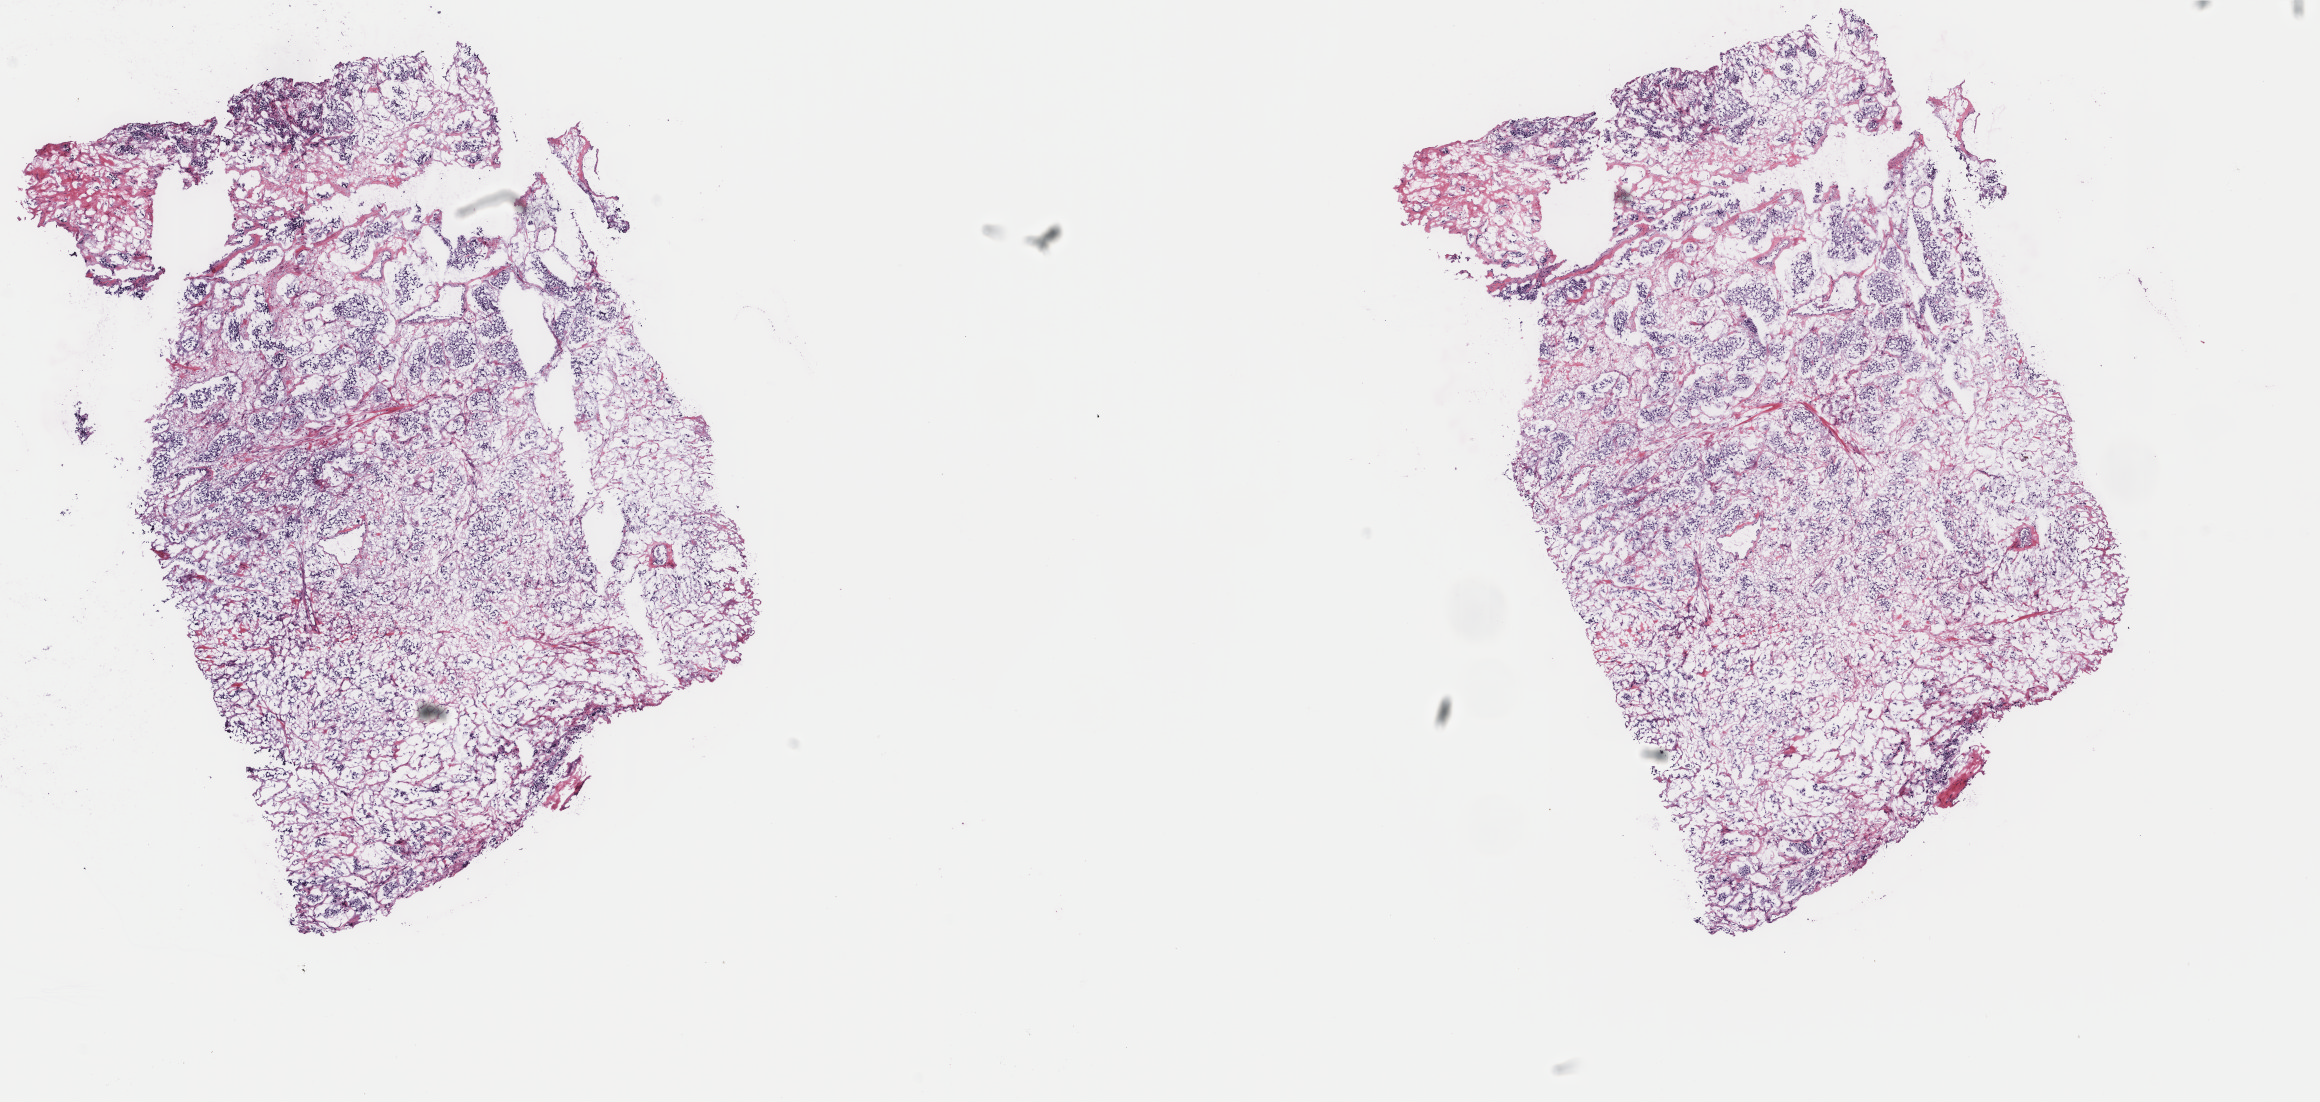
Digitized H&E-stained tissue section (whole slide), low-resolution overview of the scanned area, about 18.4 x 8.7 mm; frozen section from the top of the tissue portion; sample: primary tumour, retroperitoneum and peritoneum. Patient: male, age at initial diagnosis 65 years. Composition of this section per pathologist review: tumour cells 100%, tumour nuclei 85%, normal cells 0%, stromal cells 0%, necrosis 0%. Infiltration values recorded for this section: lymphocyte infiltration 0%, monocyte infiltration 0%, neutrophil infiltration 0%.
Diagnosis: Extra-adrenal paraganglioma, NOS (retroperitoneum). Laterality: bilateral.